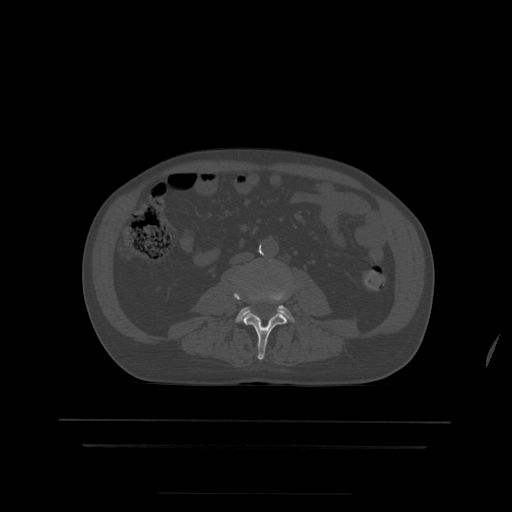
CT including the spine, one axial slice; position 110 of 522 along the scan axis; bone window (W 1800 / L 400 HU); 1.25 mm slice thickness; 512 × 512 image matrix, field of view 436 × 436 mm. Patient age 68 years. Case-level facts recorded for this patient, not image findings: primary cancer: urothelial.
Structures marked on this image (semi-automatic segmentation, software-assisted and operator-edited):
- L3 vertebra: box from (x=234, y=293) to (x=287, y=360) px
- L4 vertebra: (x=237, y=294)–(x=294, y=322)